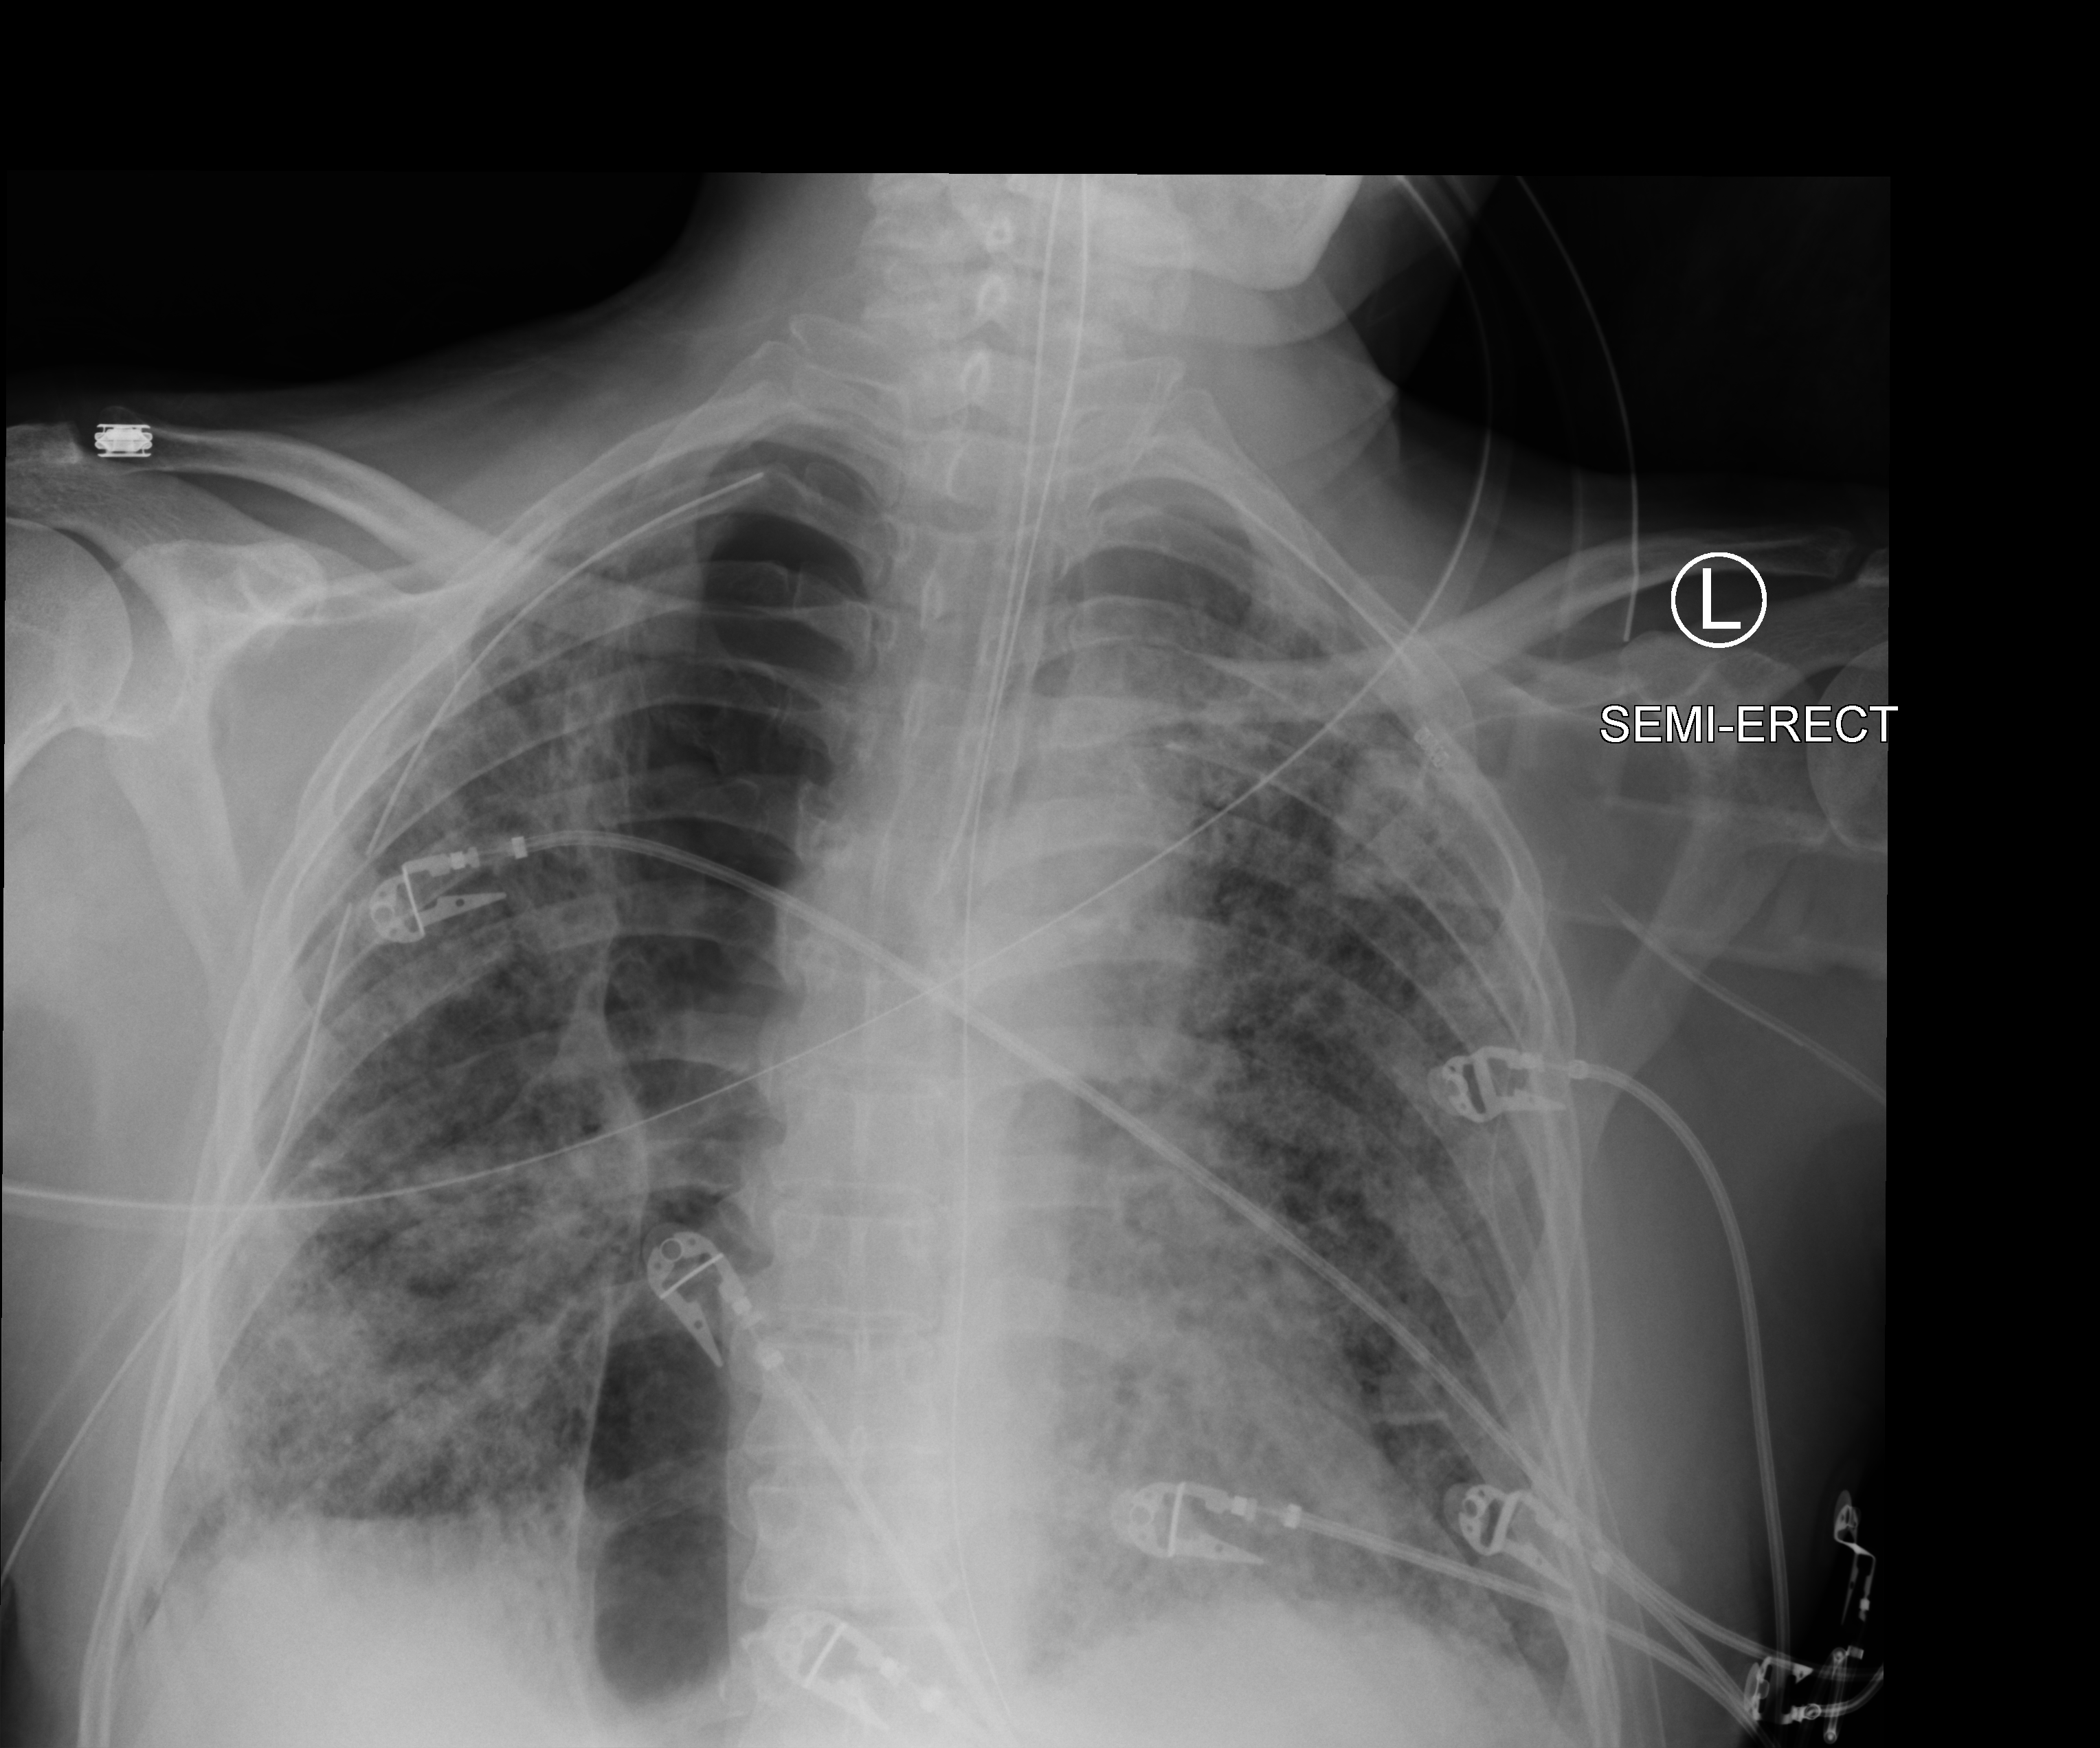
Portable chest radiograph; anteroposterior (AP) projection. Patient hospitalised with COVID-19; male, aged 60–74 years.
From the hospital-stay record, not from the radiograph (when in the stay this image was taken is not recorded):
- smoking status (admission record): never
- mechanically ventilated during this hospital stay: yes